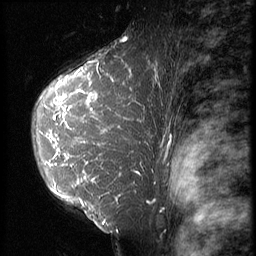
Breast MRI (dynamic contrast-enhanced), one sagittal slice; position 43 of 64 along the scan axis; 3 images stored at this slice position (order not interpretable as contrast timing); 1.5 T; TE 4.2 ms, TR 9 ms; 256 × 256 image matrix, field of view 180 × 180 mm. Patient: female, 39 years. From the clinical record (not read from this slice): setting: breast cancer imaged before/during neoadjuvant chemotherapy; receptor status: HER2-positive.
Outlined on this slice (semi-automatic segmentation, software-assisted and operator-edited):
- analysis volume of interest (the breast-tissue region the enhancement analysis was run in; not a lesion): bounding box (x1, y1, x2, y2) in pixels: (31, 47, 153, 239)
- tumour enhancement mask (voxels above the 140 % enhancement threshold inside the analysis volume of interest): (46, 60, 139, 208)